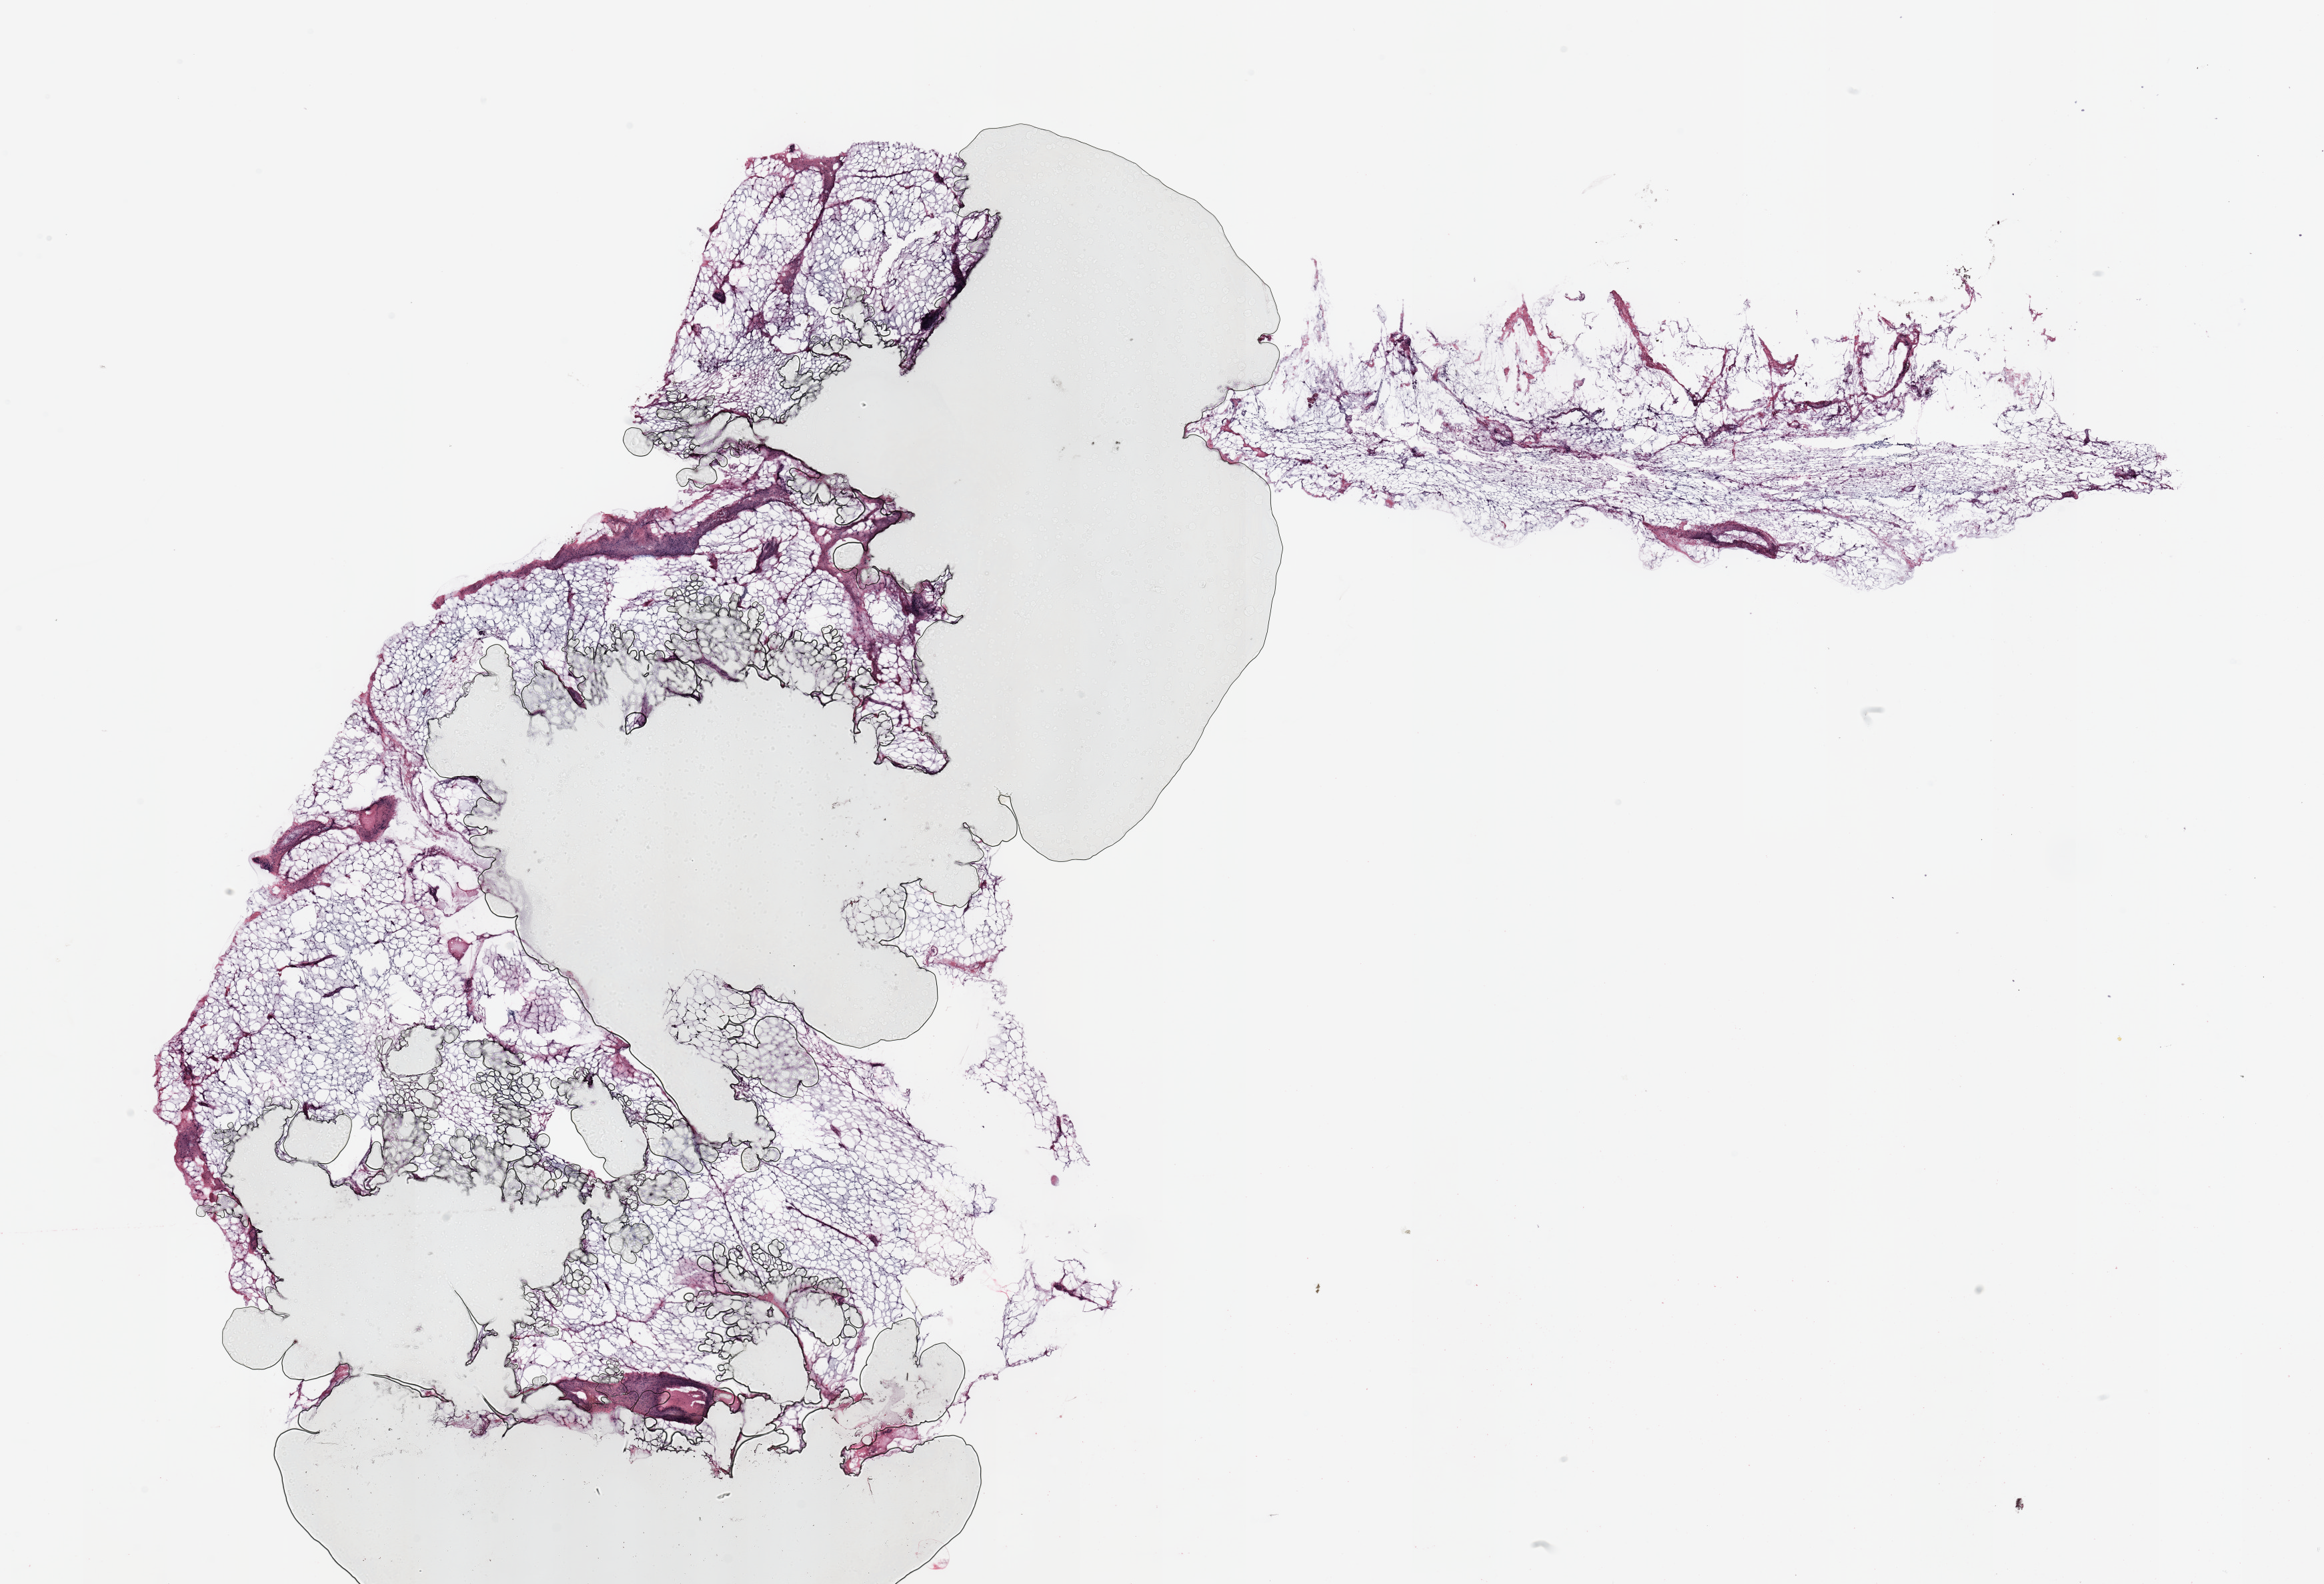
Digitized Hematoxylin and eosin (H&E) stained tissue section (whole slide) — a low-resolution overview of the entire scanned area, about 27.6 x 18.8 mm, breast, tumour tissue. Female, 58 y/o.
Histologic diagnosis: Infiltrating duct carcinoma, NOS.